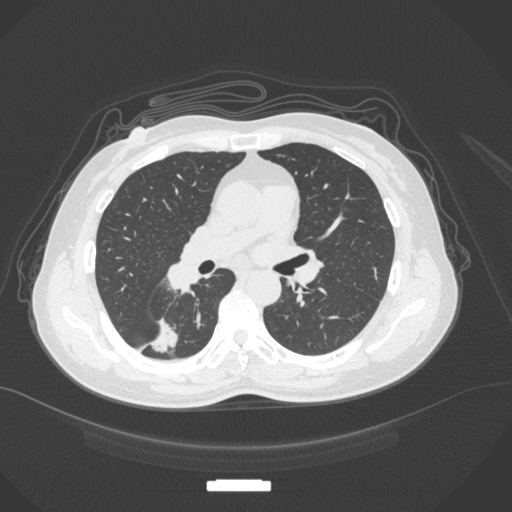
Chest CT, one axial slice. Slice 170 of 352 in the series (ordered by position). Reconstruction kernel B31f. 120 kVp. Lung window (W 1500 / L -600 HU). 1 mm slice thickness. 512 × 512 image matrix. Patient: female, 55 years. Case-level facts recorded for this patient, not image findings: clinical TNM (as recorded): T1c N1 M0.
Outlined on this slice (bounding box drawn by a radiologist):
- lung tumour (recorded histology: adenocarcinoma): bounding box (x1, y1, x2, y2) in pixels: (150, 317, 180, 360)